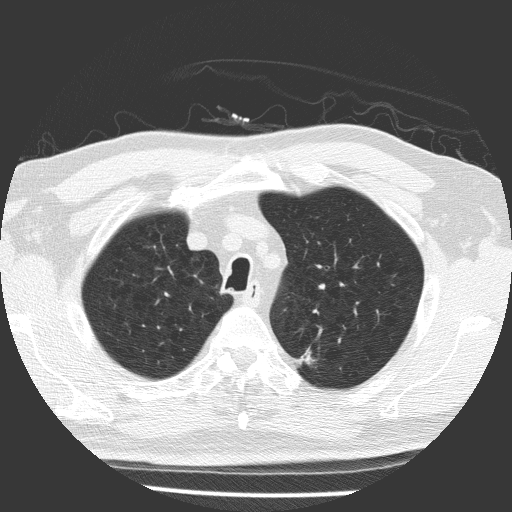
Chest CT (low-dose screening protocol), one axial image, baseline screening round, lung window (W 1500 / L -600 HU), 2 mm slice thickness, 120 kVp, 512 × 512 image matrix, field of view 323 × 323 mm. Male participant, aged 64 years at enrolment.
Lesion marked by an expert reader, bounding box <284,340,326,378> (left, top, right, bottom; pixels). Screening reader's record for this exam (one nodule recorded; not confirmed to be the boxed lesion): non-calcified nodule or mass ≥4 mm, left upper lobe, 9 × 7 mm, spiculated (stellate) margins, soft tissue attenuation. Official screen result: positive, change unspecified: nodule(s) >= 4 mm or enlarging nodule(s), mass(es), or other non-specific abnormalities suspicious for lung cancer. Participant outcome: lung cancer diagnosed 70 days after this screen — adenocarcinoma, NOS, left upper lobe, poorly differentiated (G3), stage IIA (AJCC 6th edition), 9 mm at pathology.